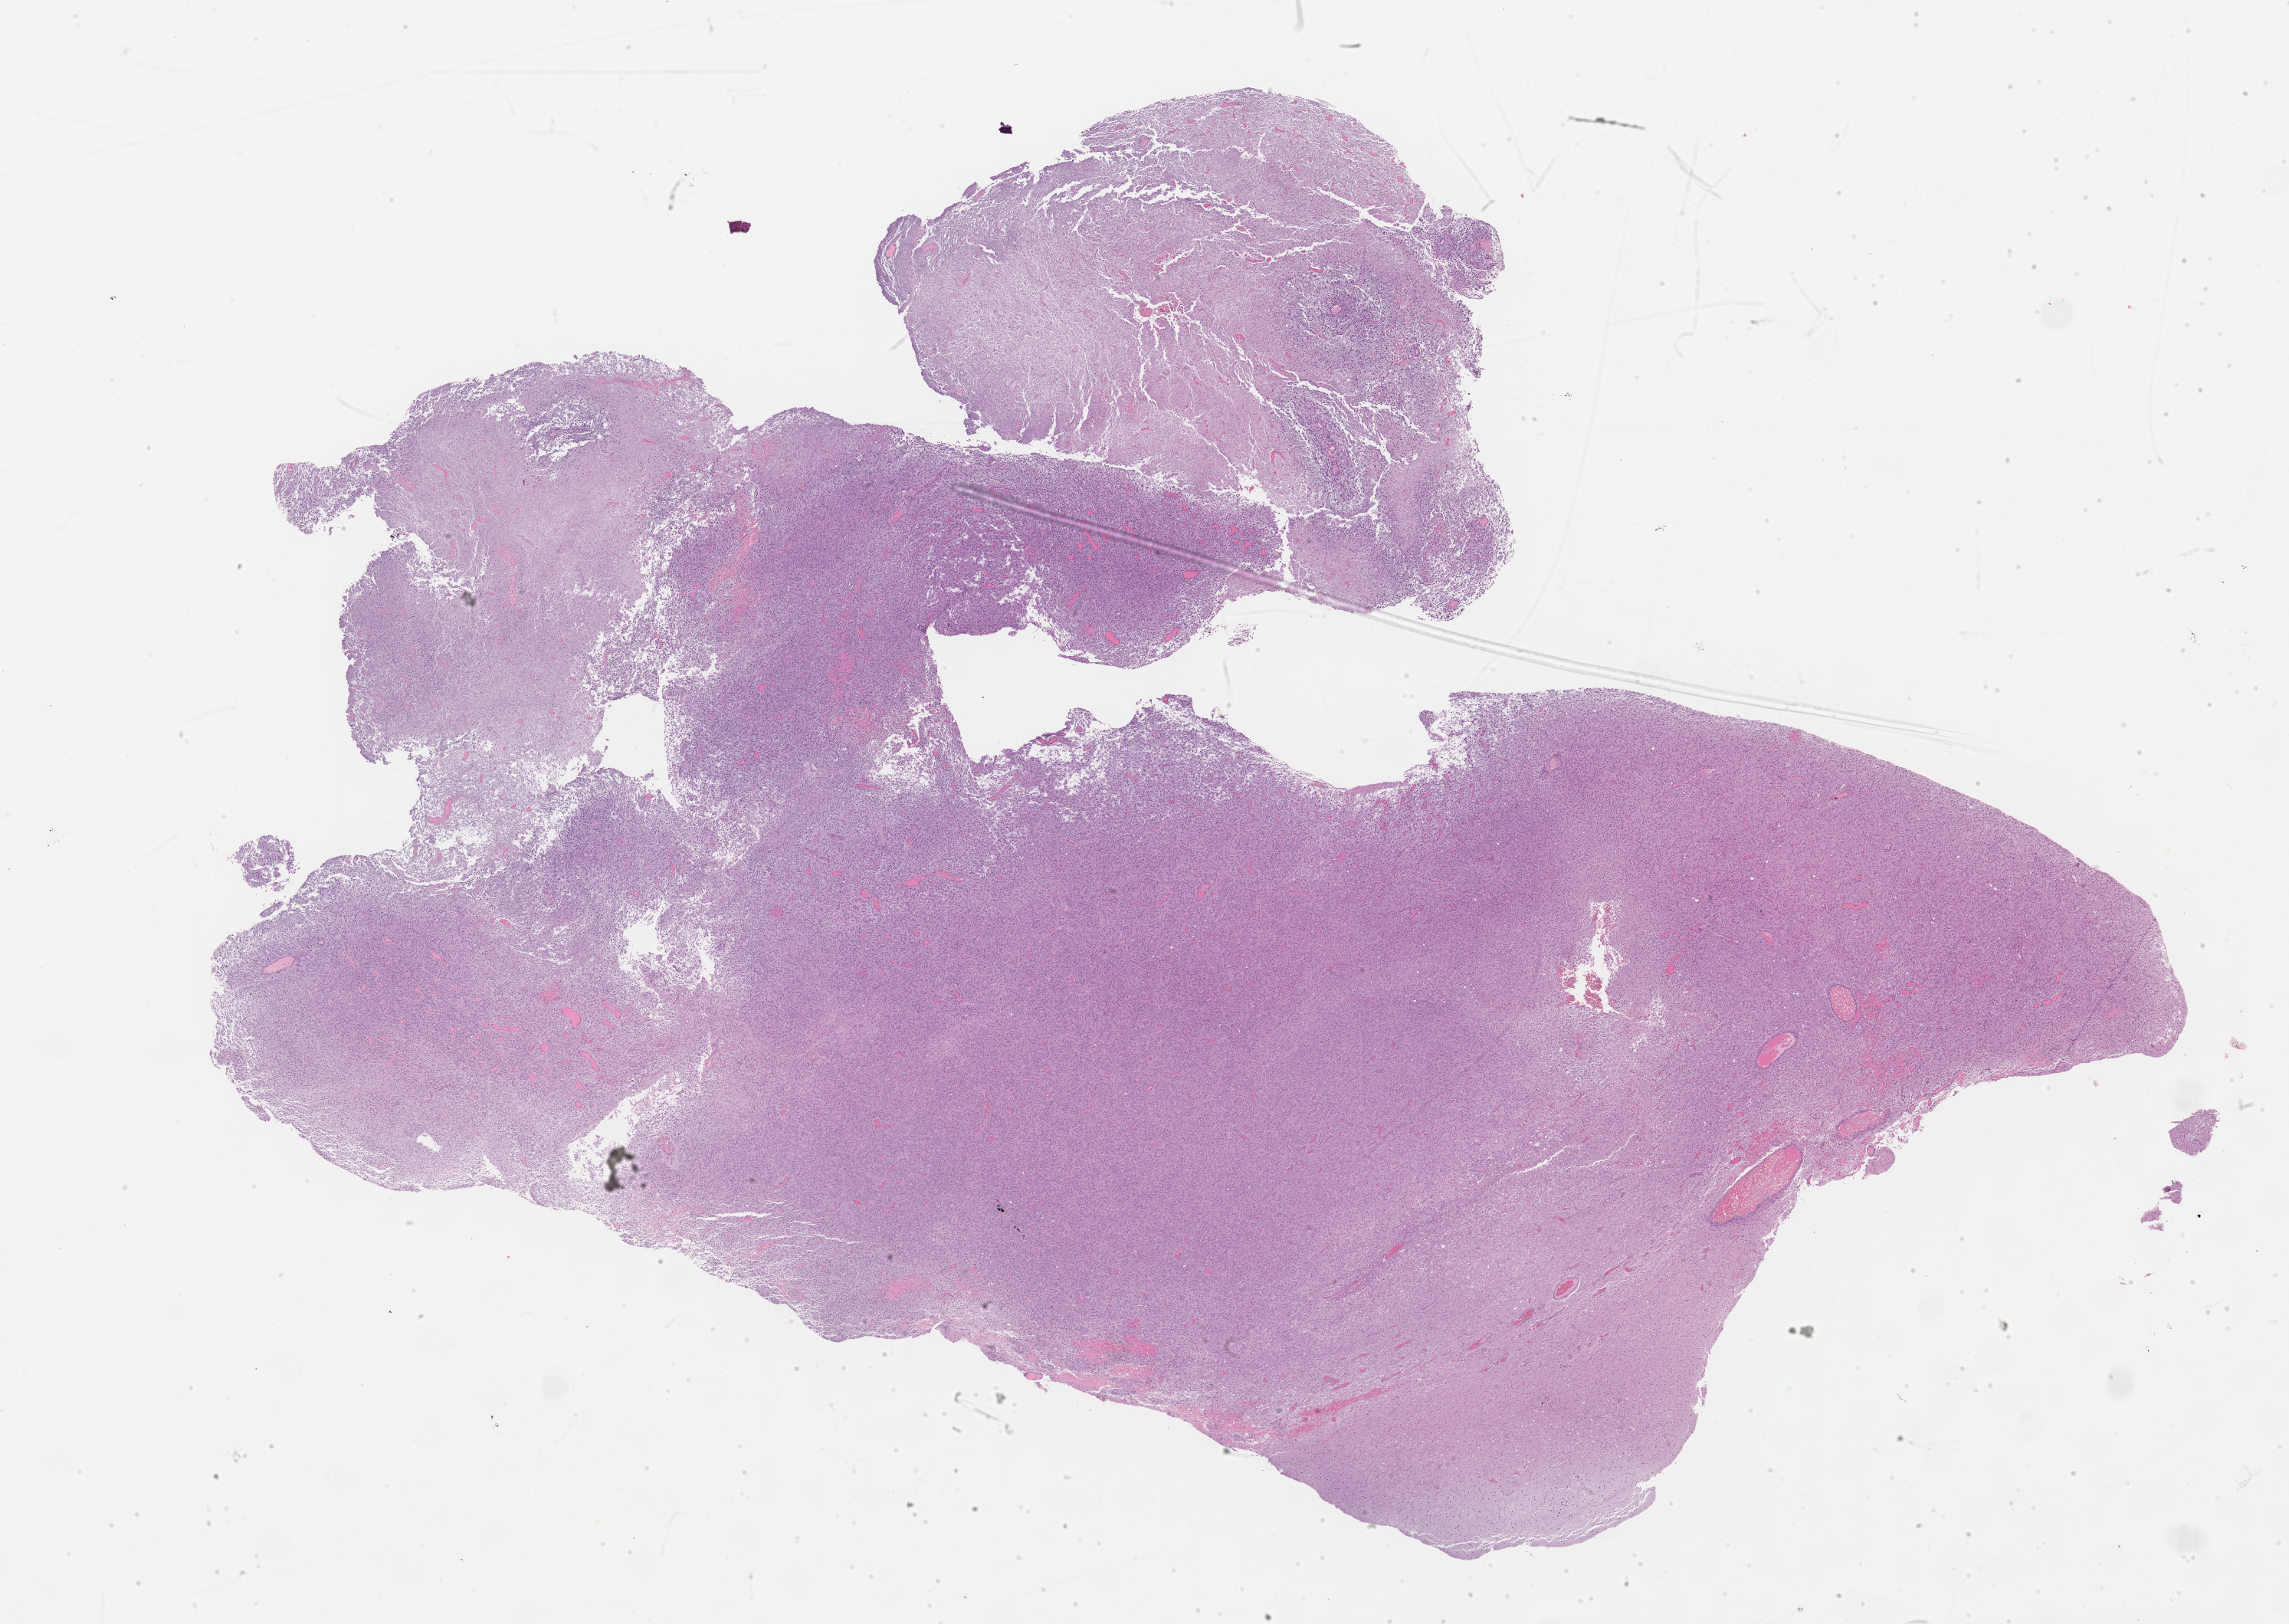
Digitized H&E-stained tissue section (whole slide) — a low-resolution overview of the entire scanned area, about 24.2 x 17.2 mm (slide scanned at 40x). Formalin-fixed paraffin-embedded (FFPE) diagnostic section. Primary tumour sample from the brain. Male, age 70 years at initial diagnosis.
- histologic diagnosis: Glioblastoma